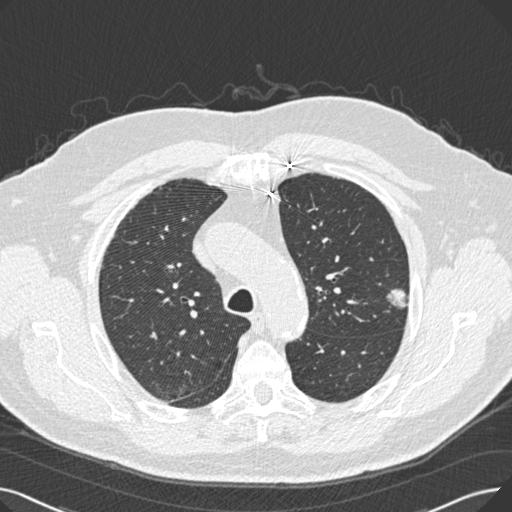
Low-dose screening chest CT, one axial slice; slice 194 of 269 in the series (ordered by position); reconstruction kernel B30f; 120 kVp; lung window (W 1500 / L -600 HU); 1 mm slice thickness; 512 × 512 image matrix, field of view 370 × 370 mm.
Annotated regions visible in this slice (outlined manually by an expert reader):
- lesion 1 (tumor, upper lobe of left lung): bounding box (x1, y1, x2, y2) in pixels: (387, 289, 408, 308)